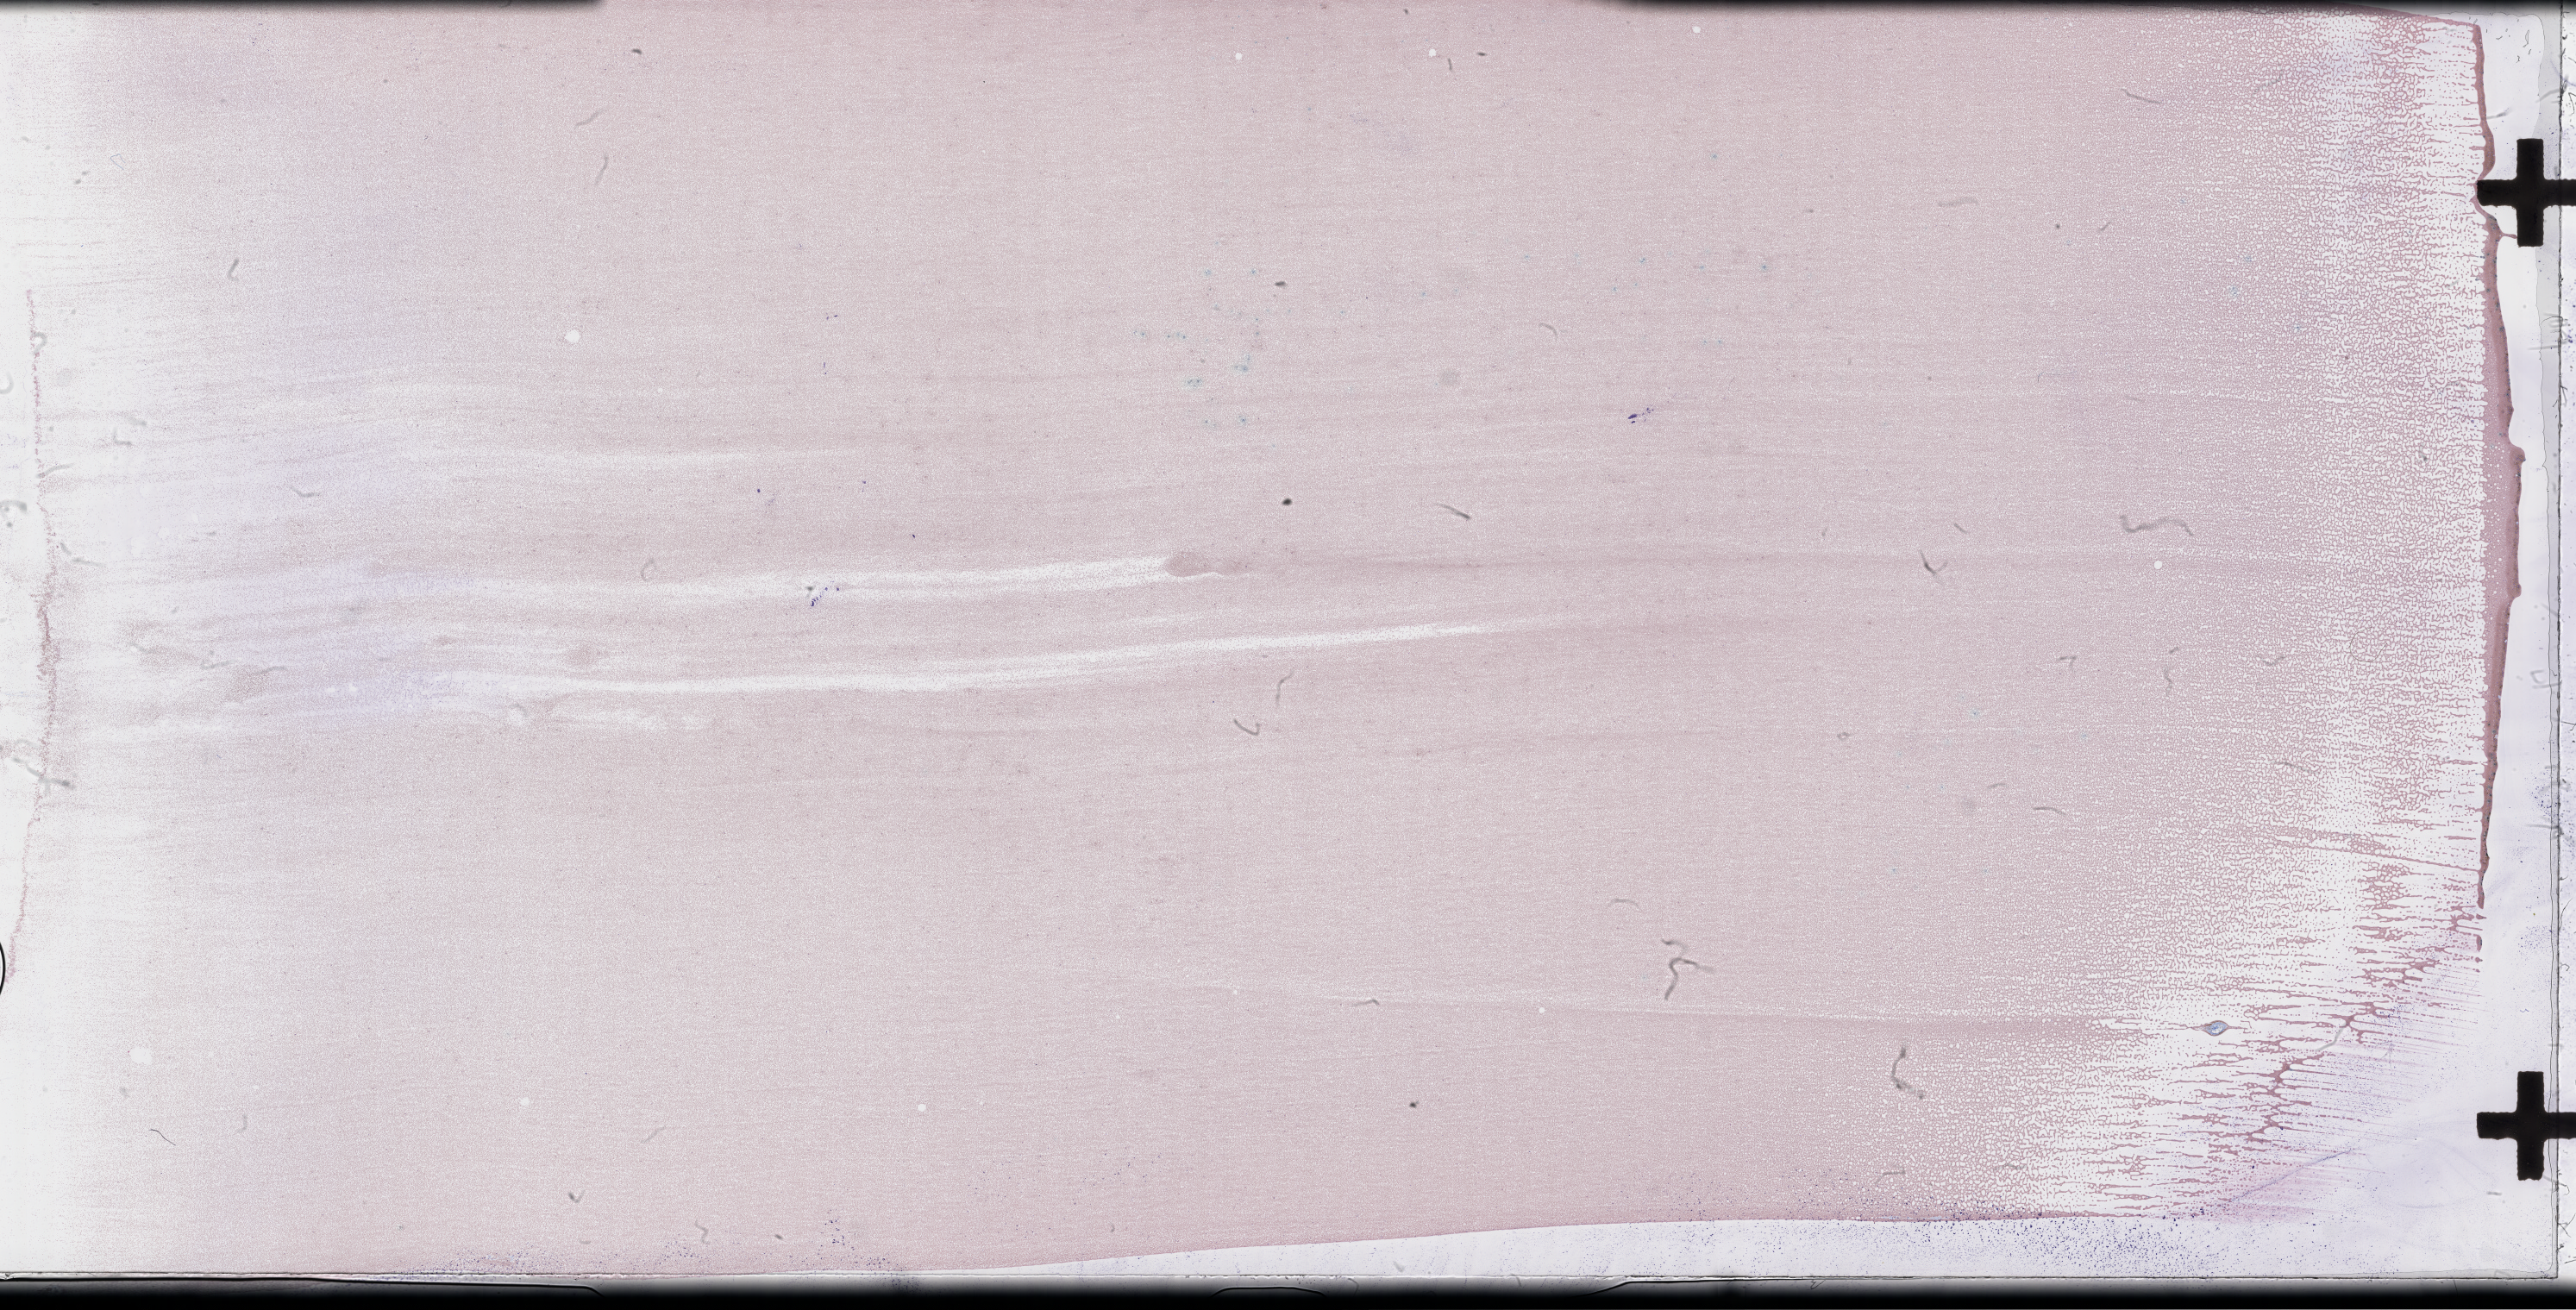
Whole-slide image of a whole blood smear, Wright–Giemsa stain — shown as a low-resolution overview of the whole scanned area (about 48.2 x 24.5 mm). Patient sex: male.
Patient diagnosis: Acute Myeloid Leukemia Not Otherwise Specified.